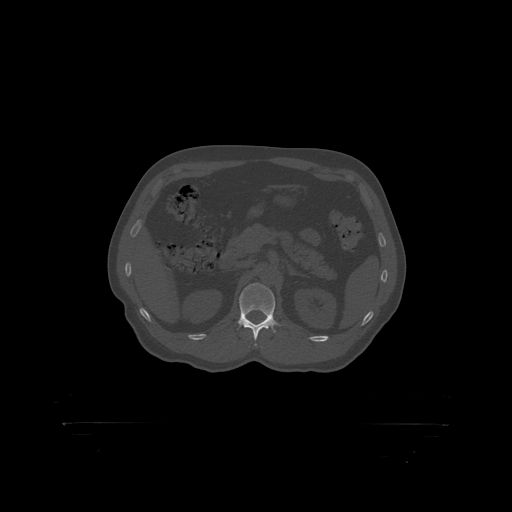
CT including the spine, one axial slice; 120 kVp; bone window (W 1800 / L 400 HU); 512 × 512 image matrix, field of view 650 × 650 mm. Male patient, age 46 years. Case-level facts recorded for this patient, not image findings: primary cancer: skin.
Outlined on this slice (semi-automatically segmented with operator editing):
- L1 vertebra: bounding box [x1, y1, x2, y2] px = [239, 283, 276, 319]